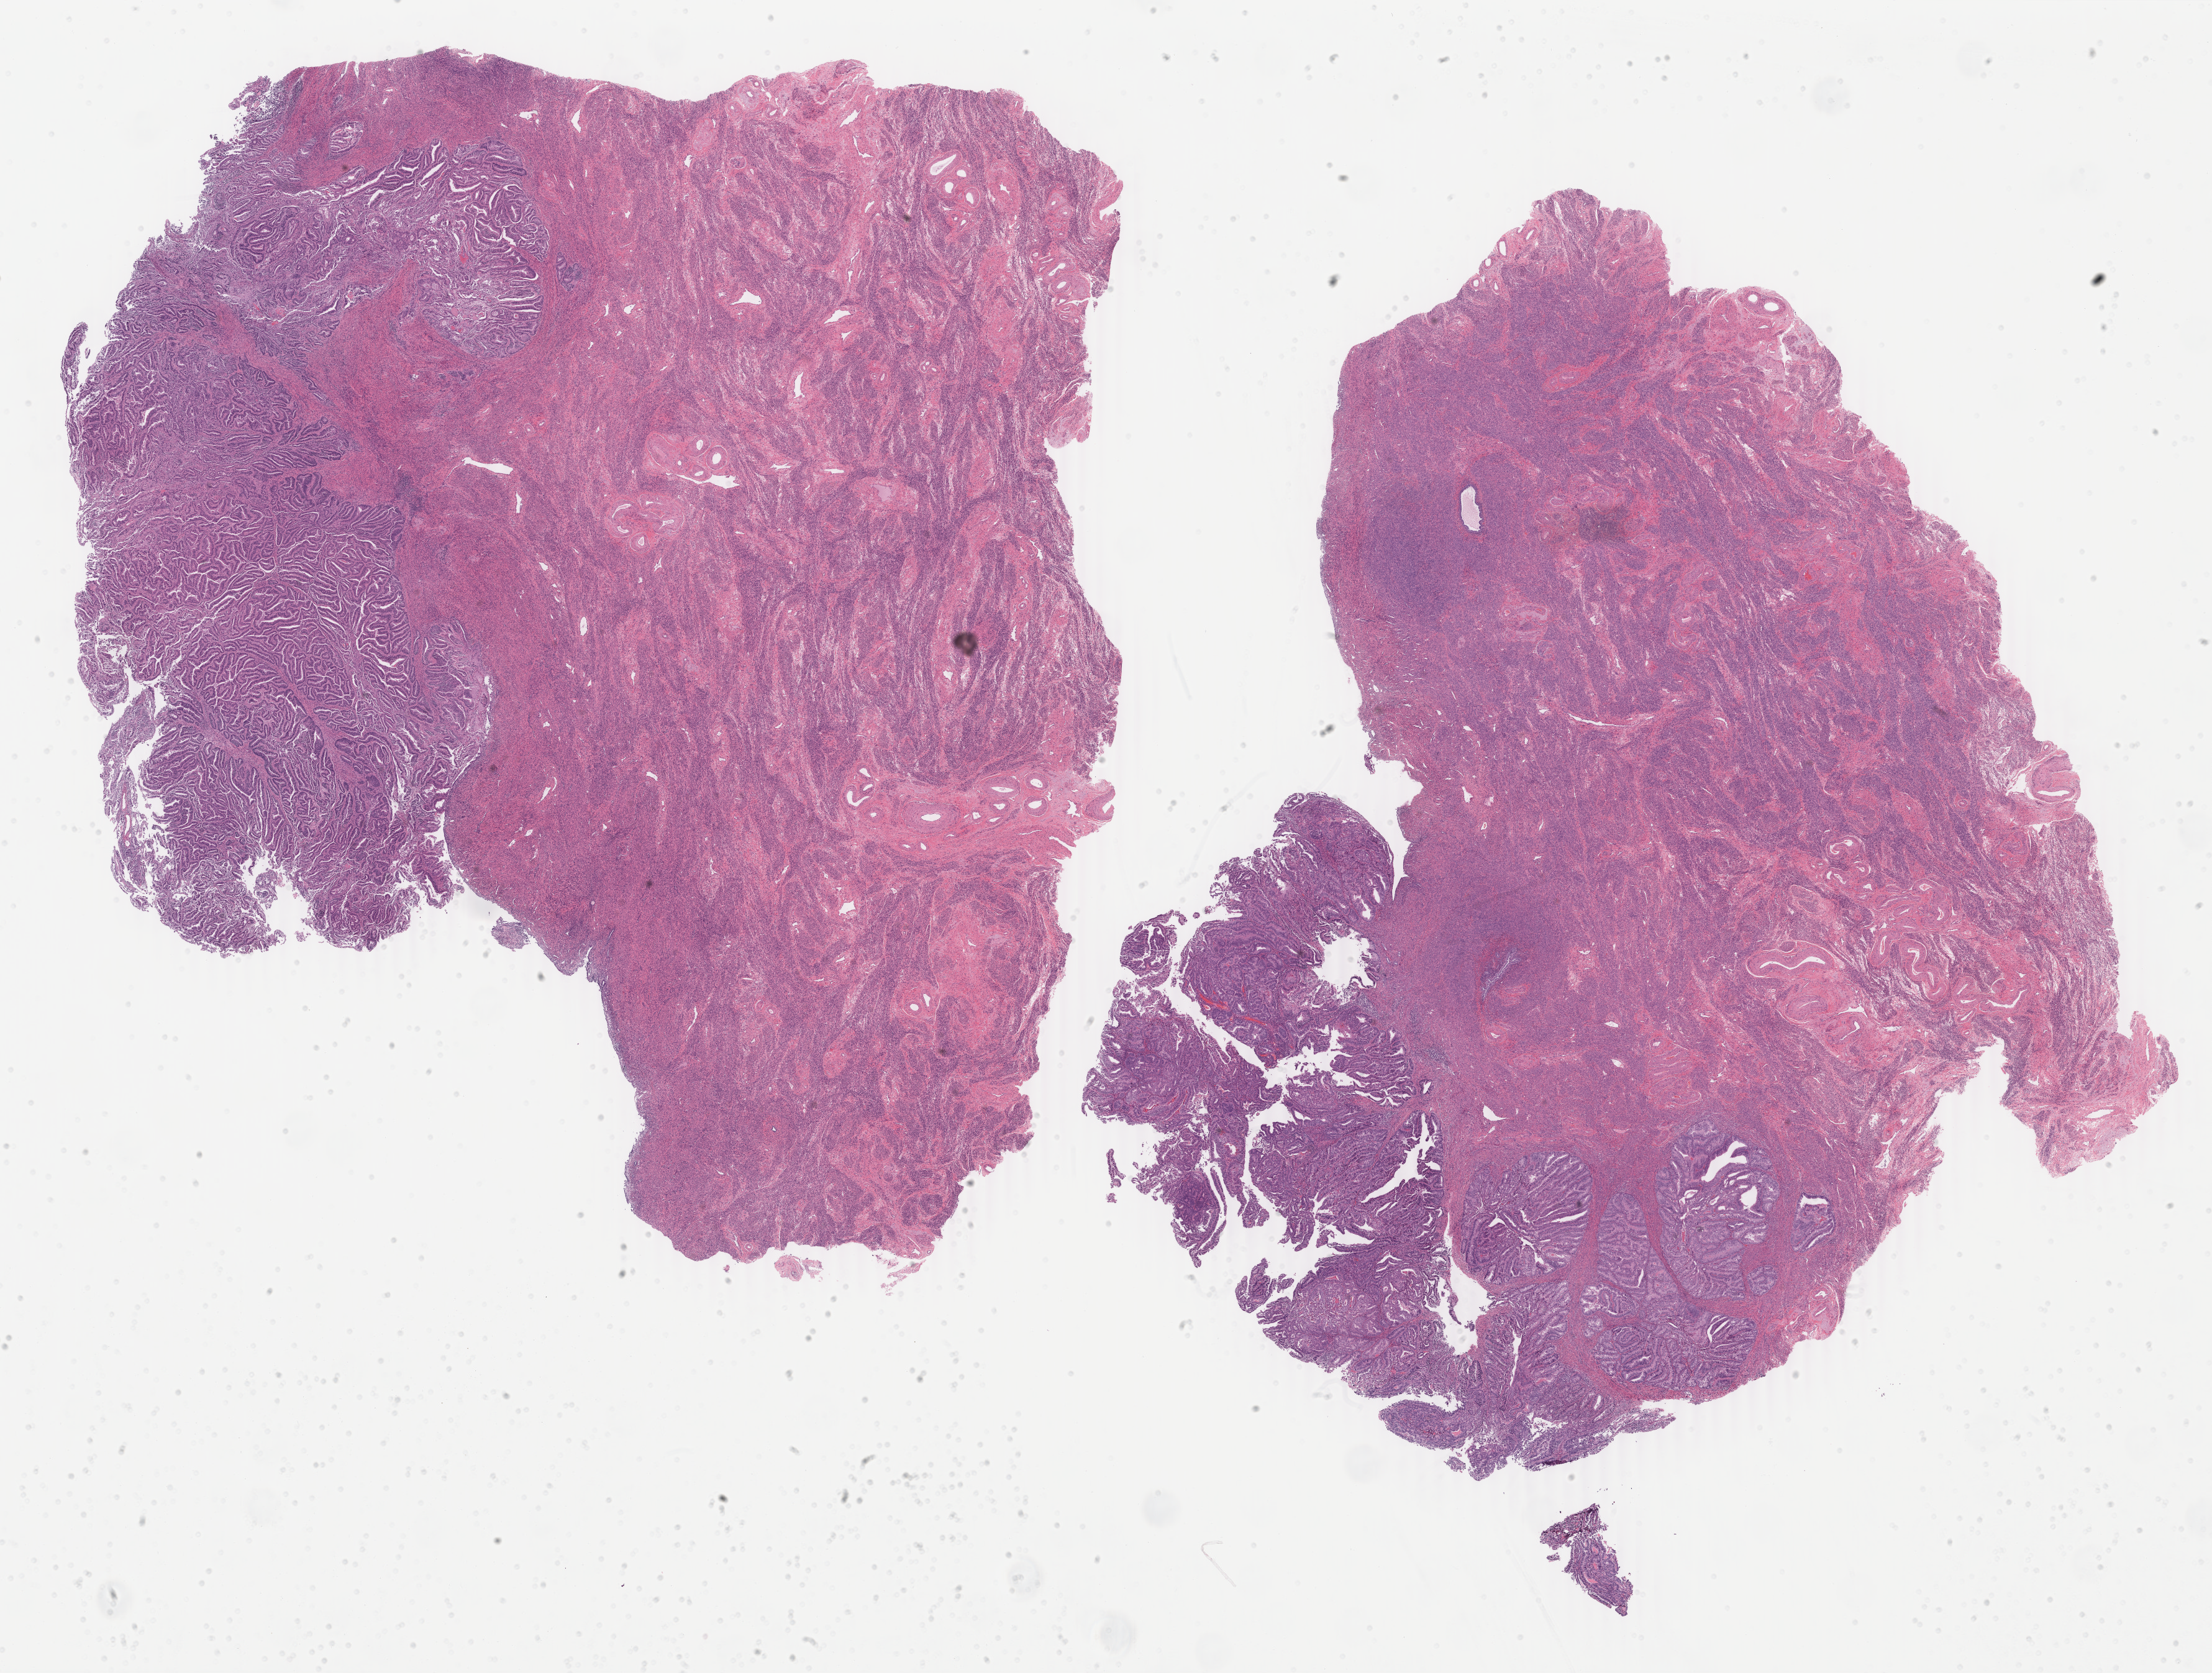
H&E whole-slide image — a low-resolution overview of the entire scanned area, about 28.3 x 21.4 mm. Formalin-fixed paraffin-embedded (FFPE) diagnostic section. Sample: primary tumour, uterus. Female patient; age at initial diagnosis 87 years. Histologic grade: G1 (well differentiated).
* diagnosis: Endometrioid adenocarcinoma, NOS (endometrium)
* FIGO stage: IB